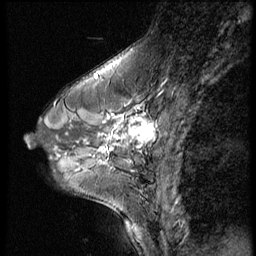
Breast MRI (dynamic contrast-enhanced), one sagittal slice; slice 21 of 56 in the series (ordered by position); dynamic contrast-enhanced series, image 2 of 3 at this slice position (ordered by acquisition); 1.5 T; TE 4.2 ms, TR 9 ms; 2.5 mm slice thickness; 256 × 256 image matrix, field of view 180 × 180 mm. Patient: female, 46 years. From the clinical record (not read from this slice): setting: breast cancer imaged before/during neoadjuvant chemotherapy; receptor status: HER2-positive.
Structures marked on this image (semi-automatic segmentation, software-assisted and operator-edited):
- analysis volume of interest (the breast-tissue region the enhancement analysis was run in; not a lesion): bounding box (x1, y1, x2, y2) in pixels: (64, 98, 174, 182)
- tumour enhancement mask (voxels above the 140 % enhancement threshold inside the analysis volume of interest): (104, 115, 156, 152)